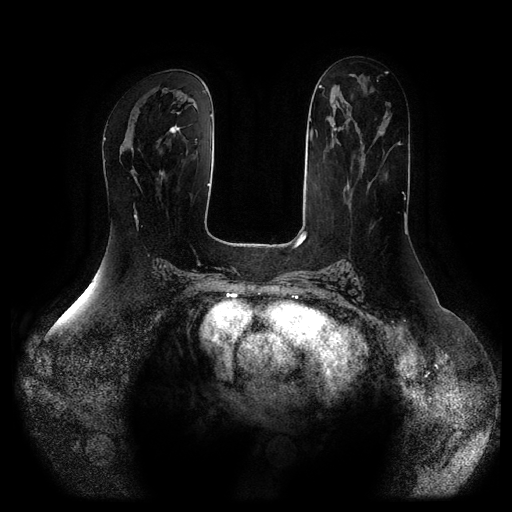
Breast MRI (dynamic contrast-enhanced, multi-phase), one axial slice; position 46 of 116 along the scan axis; dynamic contrast-enhanced series, time point 2 of 5 at this slice position (early post-contrast); 1.5 T; TE 2.5 ms, TR 5.2 ms; 2 mm slice thickness; 512 × 512 image matrix, field of view 400 × 400 mm. Female patient, age 66 years.
Structures marked on this image (semi-automatically segmented with operator editing):
- breast lesion (labelled 'tumour' in the annotation; benign lesions carry a separate 'benign' label): box from (x=169, y=124) to (x=183, y=136) px